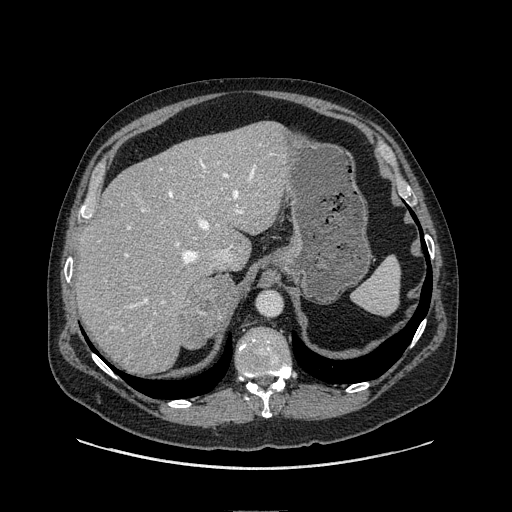
Contrast-enhanced abdominal CT, one axial slice. Position 82 of 149 along the scan axis. Soft-tissue window (W 400 / L 40 HU). 1.25 mm slice thickness. 512 × 512 image matrix. Male patient. From the clinical record (not read from this slice): diagnosis: adrenocortical carcinoma; tumour side: right adrenal; tumour size at pathology: 7.5 cm; Ki-67 index: 15 %; stage (as recorded): 2.
Annotated regions visible in this slice (semi-automatically segmented with operator editing):
- mass: bounding box <183,272,238,346> (left, top, right, bottom; pixels)